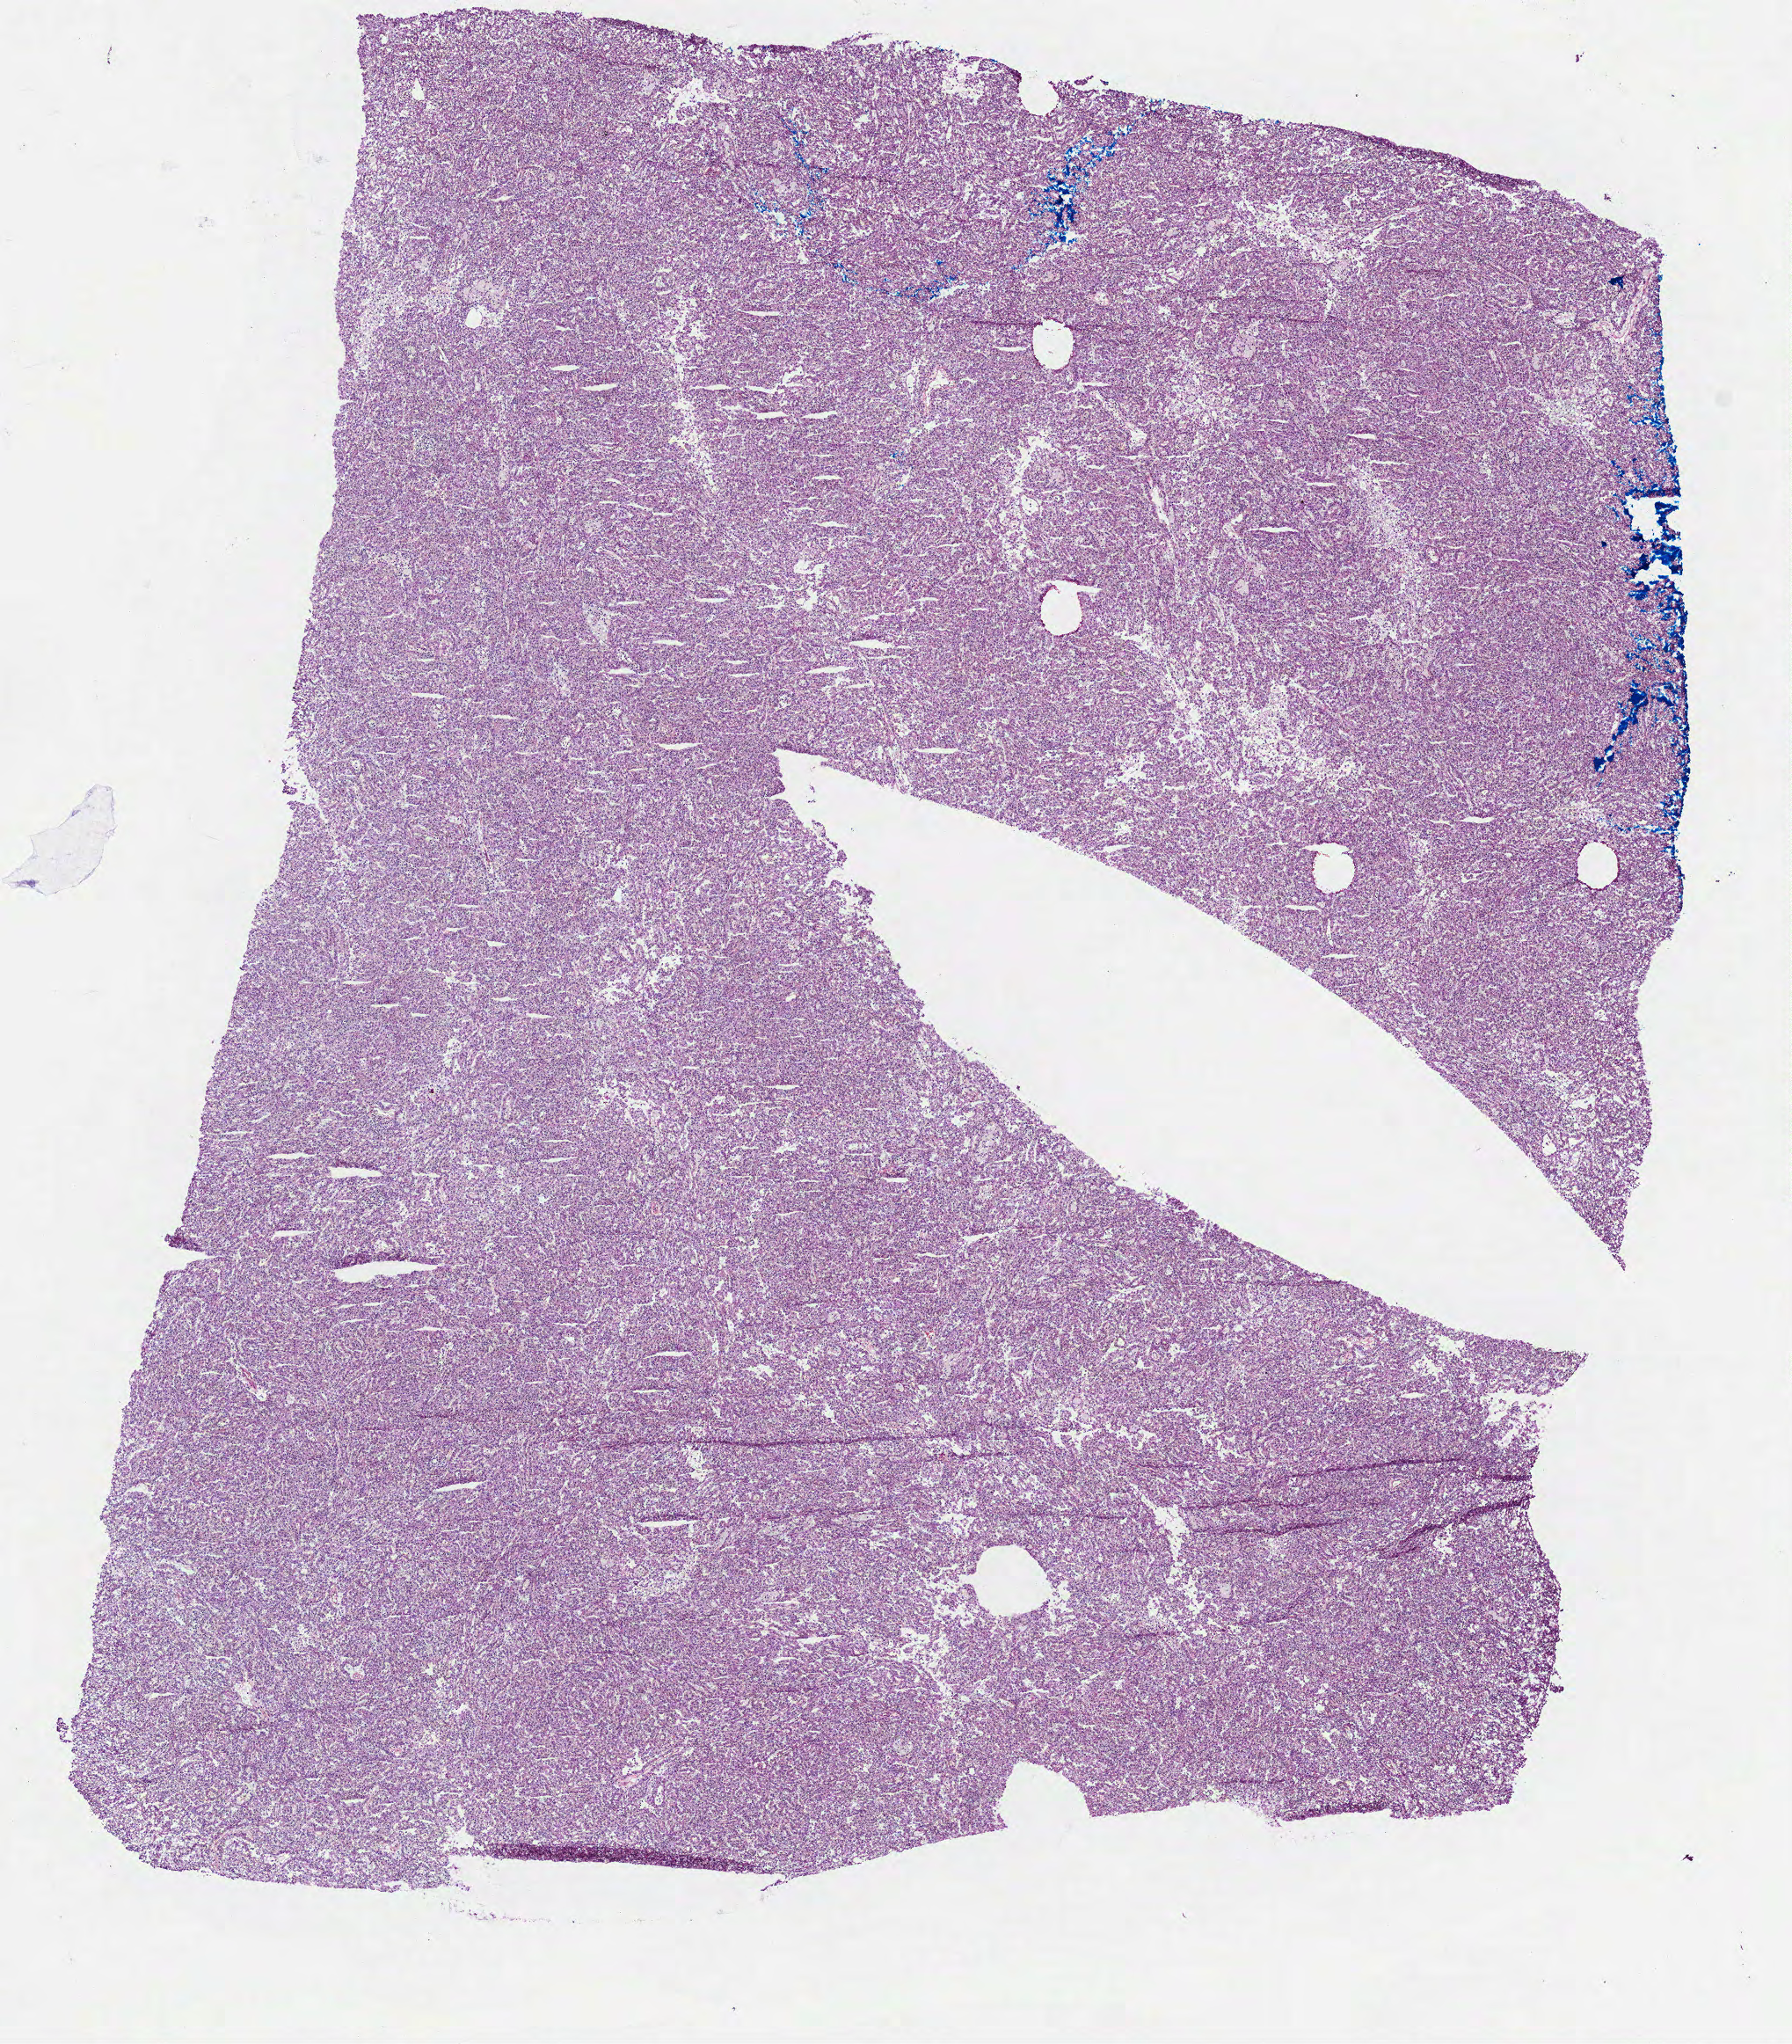
Digitized H&E tissue section (whole slide) — a low-resolution overview of the entire scanned area, about 8.2 x 9.4 mm, frozen section from the bottom of the tissue portion, primary tumour sample from the kidney. Male, age 60 years at initial diagnosis. Slide review estimates, as recorded: tumour cells 95%, tumour nuclei 80%, normal cells 0%, stromal cells 5%, necrosis 0%.
- laterality: left
- TNM: T1 N0 M0
- AJCC pathologic stage: I (7th edition)
- histologic diagnosis: Papillary adenocarcinoma, NOS